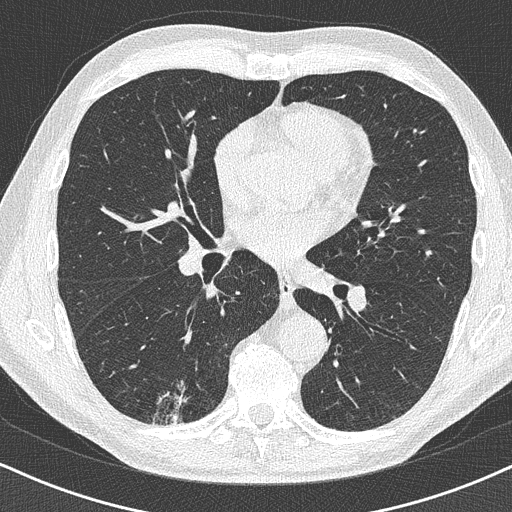
Chest CT (low-dose screening protocol), one axial image, first (baseline) screen, lung window (W 1500 / L -600 HU), 1 mm slice thickness. Male participant, aged 63 years at enrolment. Former smoker at enrolment.
Lesion marked by an expert reader, bounding box <133,365,205,429> (left, top, right, bottom; pixels). Screening reader's record for this exam (one nodule recorded; not confirmed to be the boxed lesion): non-calcified nodule or mass ≥4 mm, right lower lobe, 16 × 13 mm, poorly defined margins. Official screen result: positive, change unspecified: nodule(s) >= 4 mm or enlarging nodule(s), mass(es), or other non-specific abnormalities suspicious for lung cancer. Lung cancer was diagnosed 74 days after this screen: adenocarcinoma, NOS, right lower lobe, moderately differentiated (G2), stage IA (AJCC 6th edition), 20 mm at pathology.